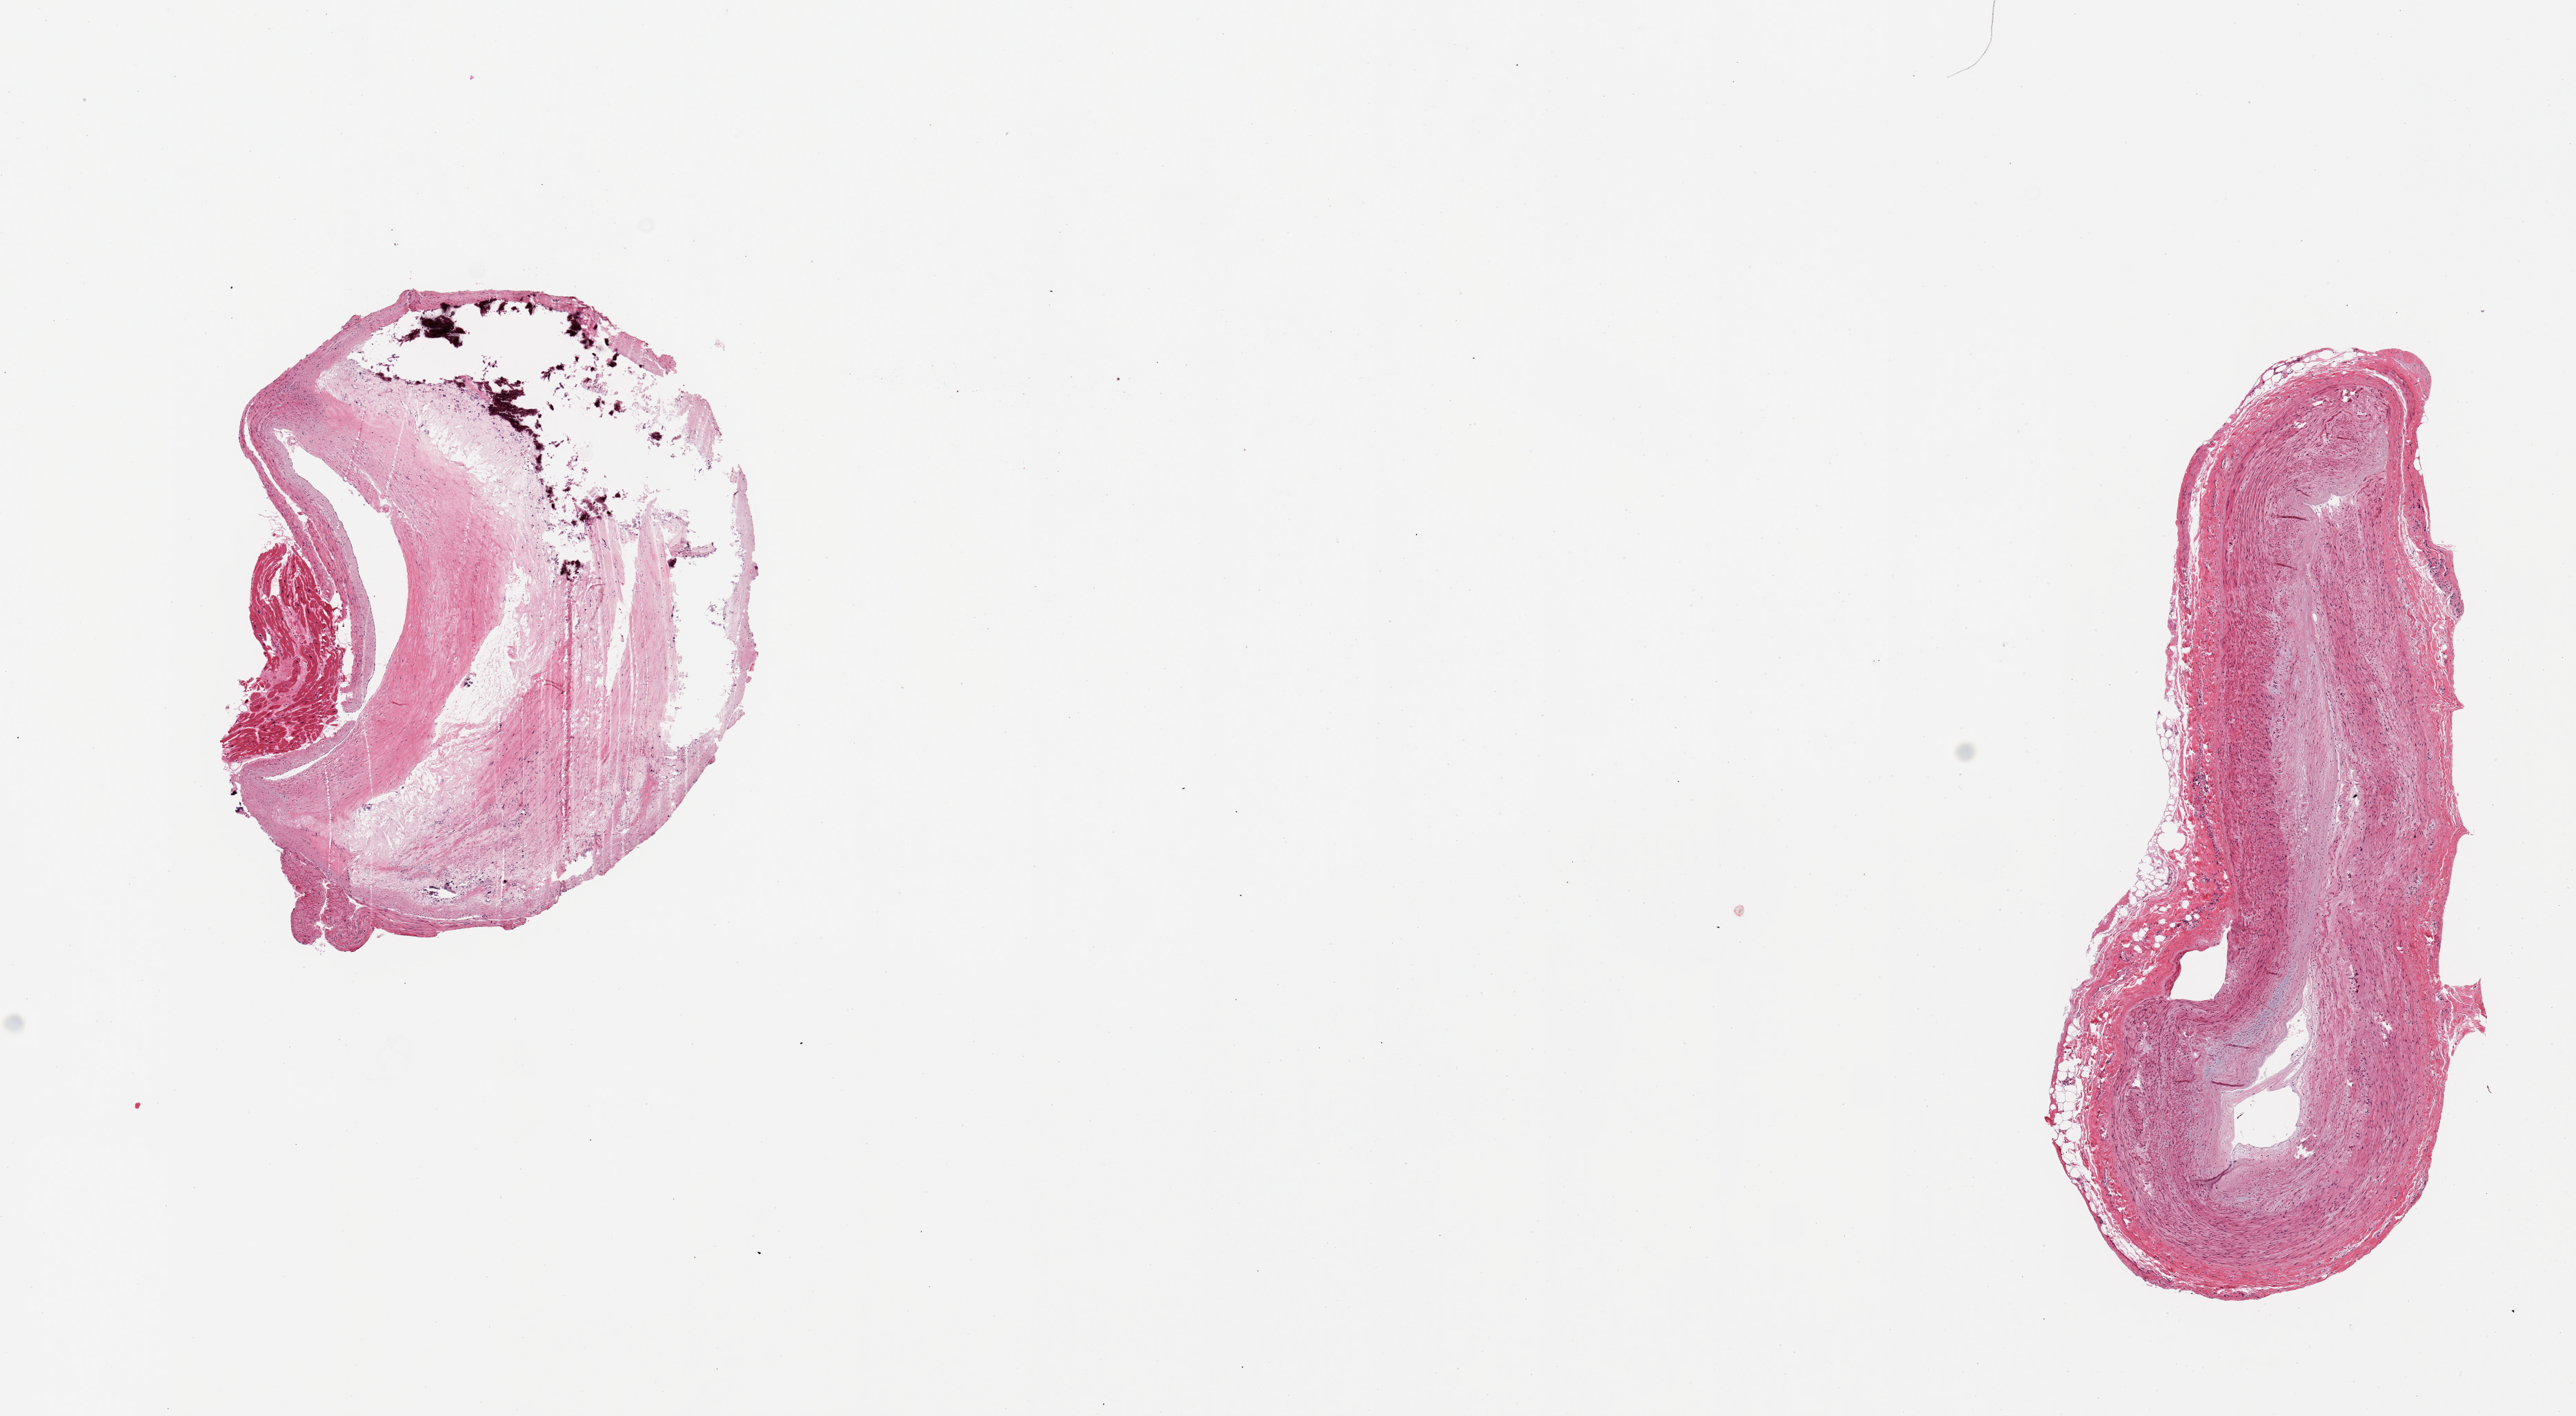
Digitized H&E-stained section — whole scanned area (about 14.8 x 8.1 mm) shown as a low-resolution overview; PAXgene-fixed, paraffin-embedded tissue; target tissue: coronary artery; tissue donor sample. Male donor.
Reviewer comment on this tissue sample: 2 pieces; severe calcific atherosclerosis, fragment of myocardium.